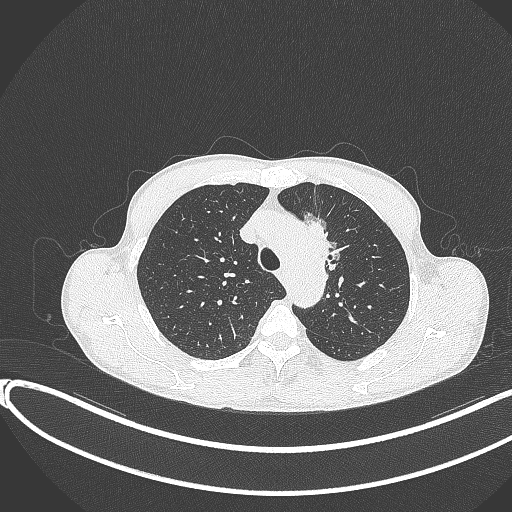
Chest CT, one axial slice; slice 288 of 374 in the series (ordered by position); reconstruction kernel B70f; 120 kVp; lung window (W 1500 / L -600 HU); 512 × 512 image matrix. Patient: male, 58 years. From the clinical record (not read from this slice): clinical TNM (as recorded): T1c N1 M0.
Annotated regions visible in this slice (bounding box drawn by a radiologist):
- lung tumour (recorded histology: adenocarcinoma): bounding box [x1, y1, x2, y2] px = [295, 209, 338, 286]